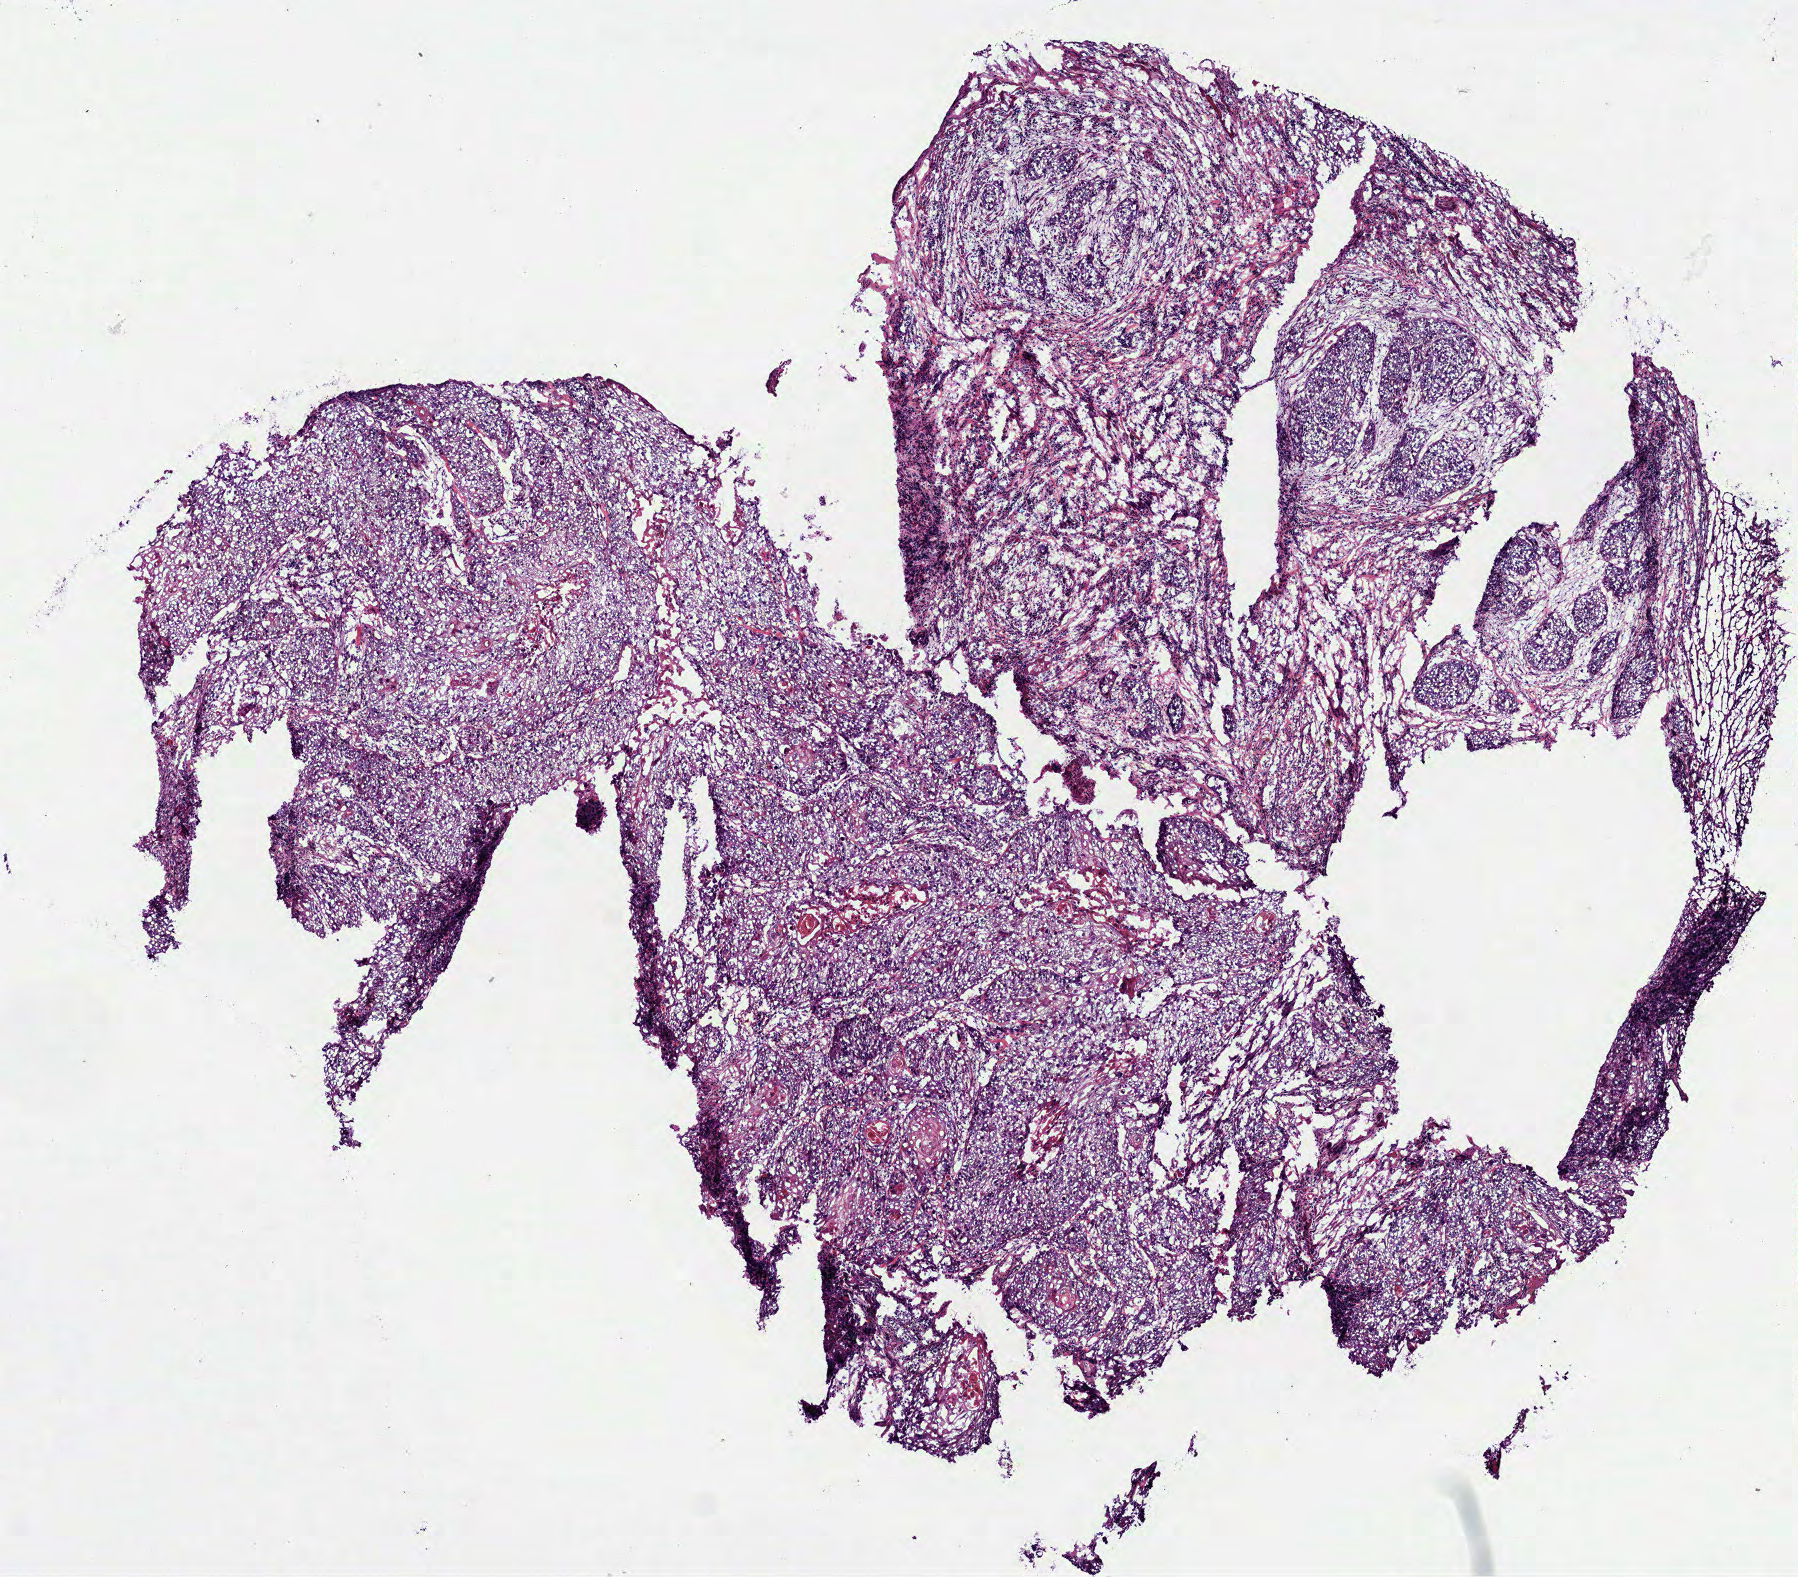
Whole-slide histology image, H&E — low-resolution overview of the scanned area, about 7.3 x 6.4 mm (from a 40x scan), frozen section, head and neck, primary tumour sample. Female patient; age at initial diagnosis 50 years. Histologic grade: G2 (moderately differentiated). Composition of this section per pathologist review: tumour cells 85%, tumour nuclei 85%, normal cells 0%, stromal cells 15%, necrosis 0%.
• AJCC pathologic stage: III (7th edition)
• pathologic diagnosis: Squamous cell carcinoma, NOS (tongue, NOS)